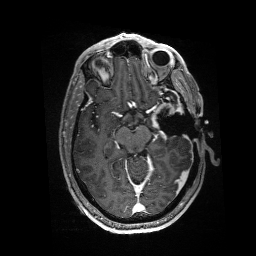
Brain MRI from a brain-tumour surgery series, one axial slice; position 97 of 176 along the scan axis; T1-weighted post-contrast; 256 × 256 image matrix, field of view 256 × 256 mm. Case-level facts recorded for this patient, not image findings: histopathology: Glioblastoma; WHO grade: 4; IDH mutation: no.
Structures marked on this image (manually delineated by an expert):
- residual tumour: bounding box <151,103,184,128> (left, top, right, bottom; pixels)